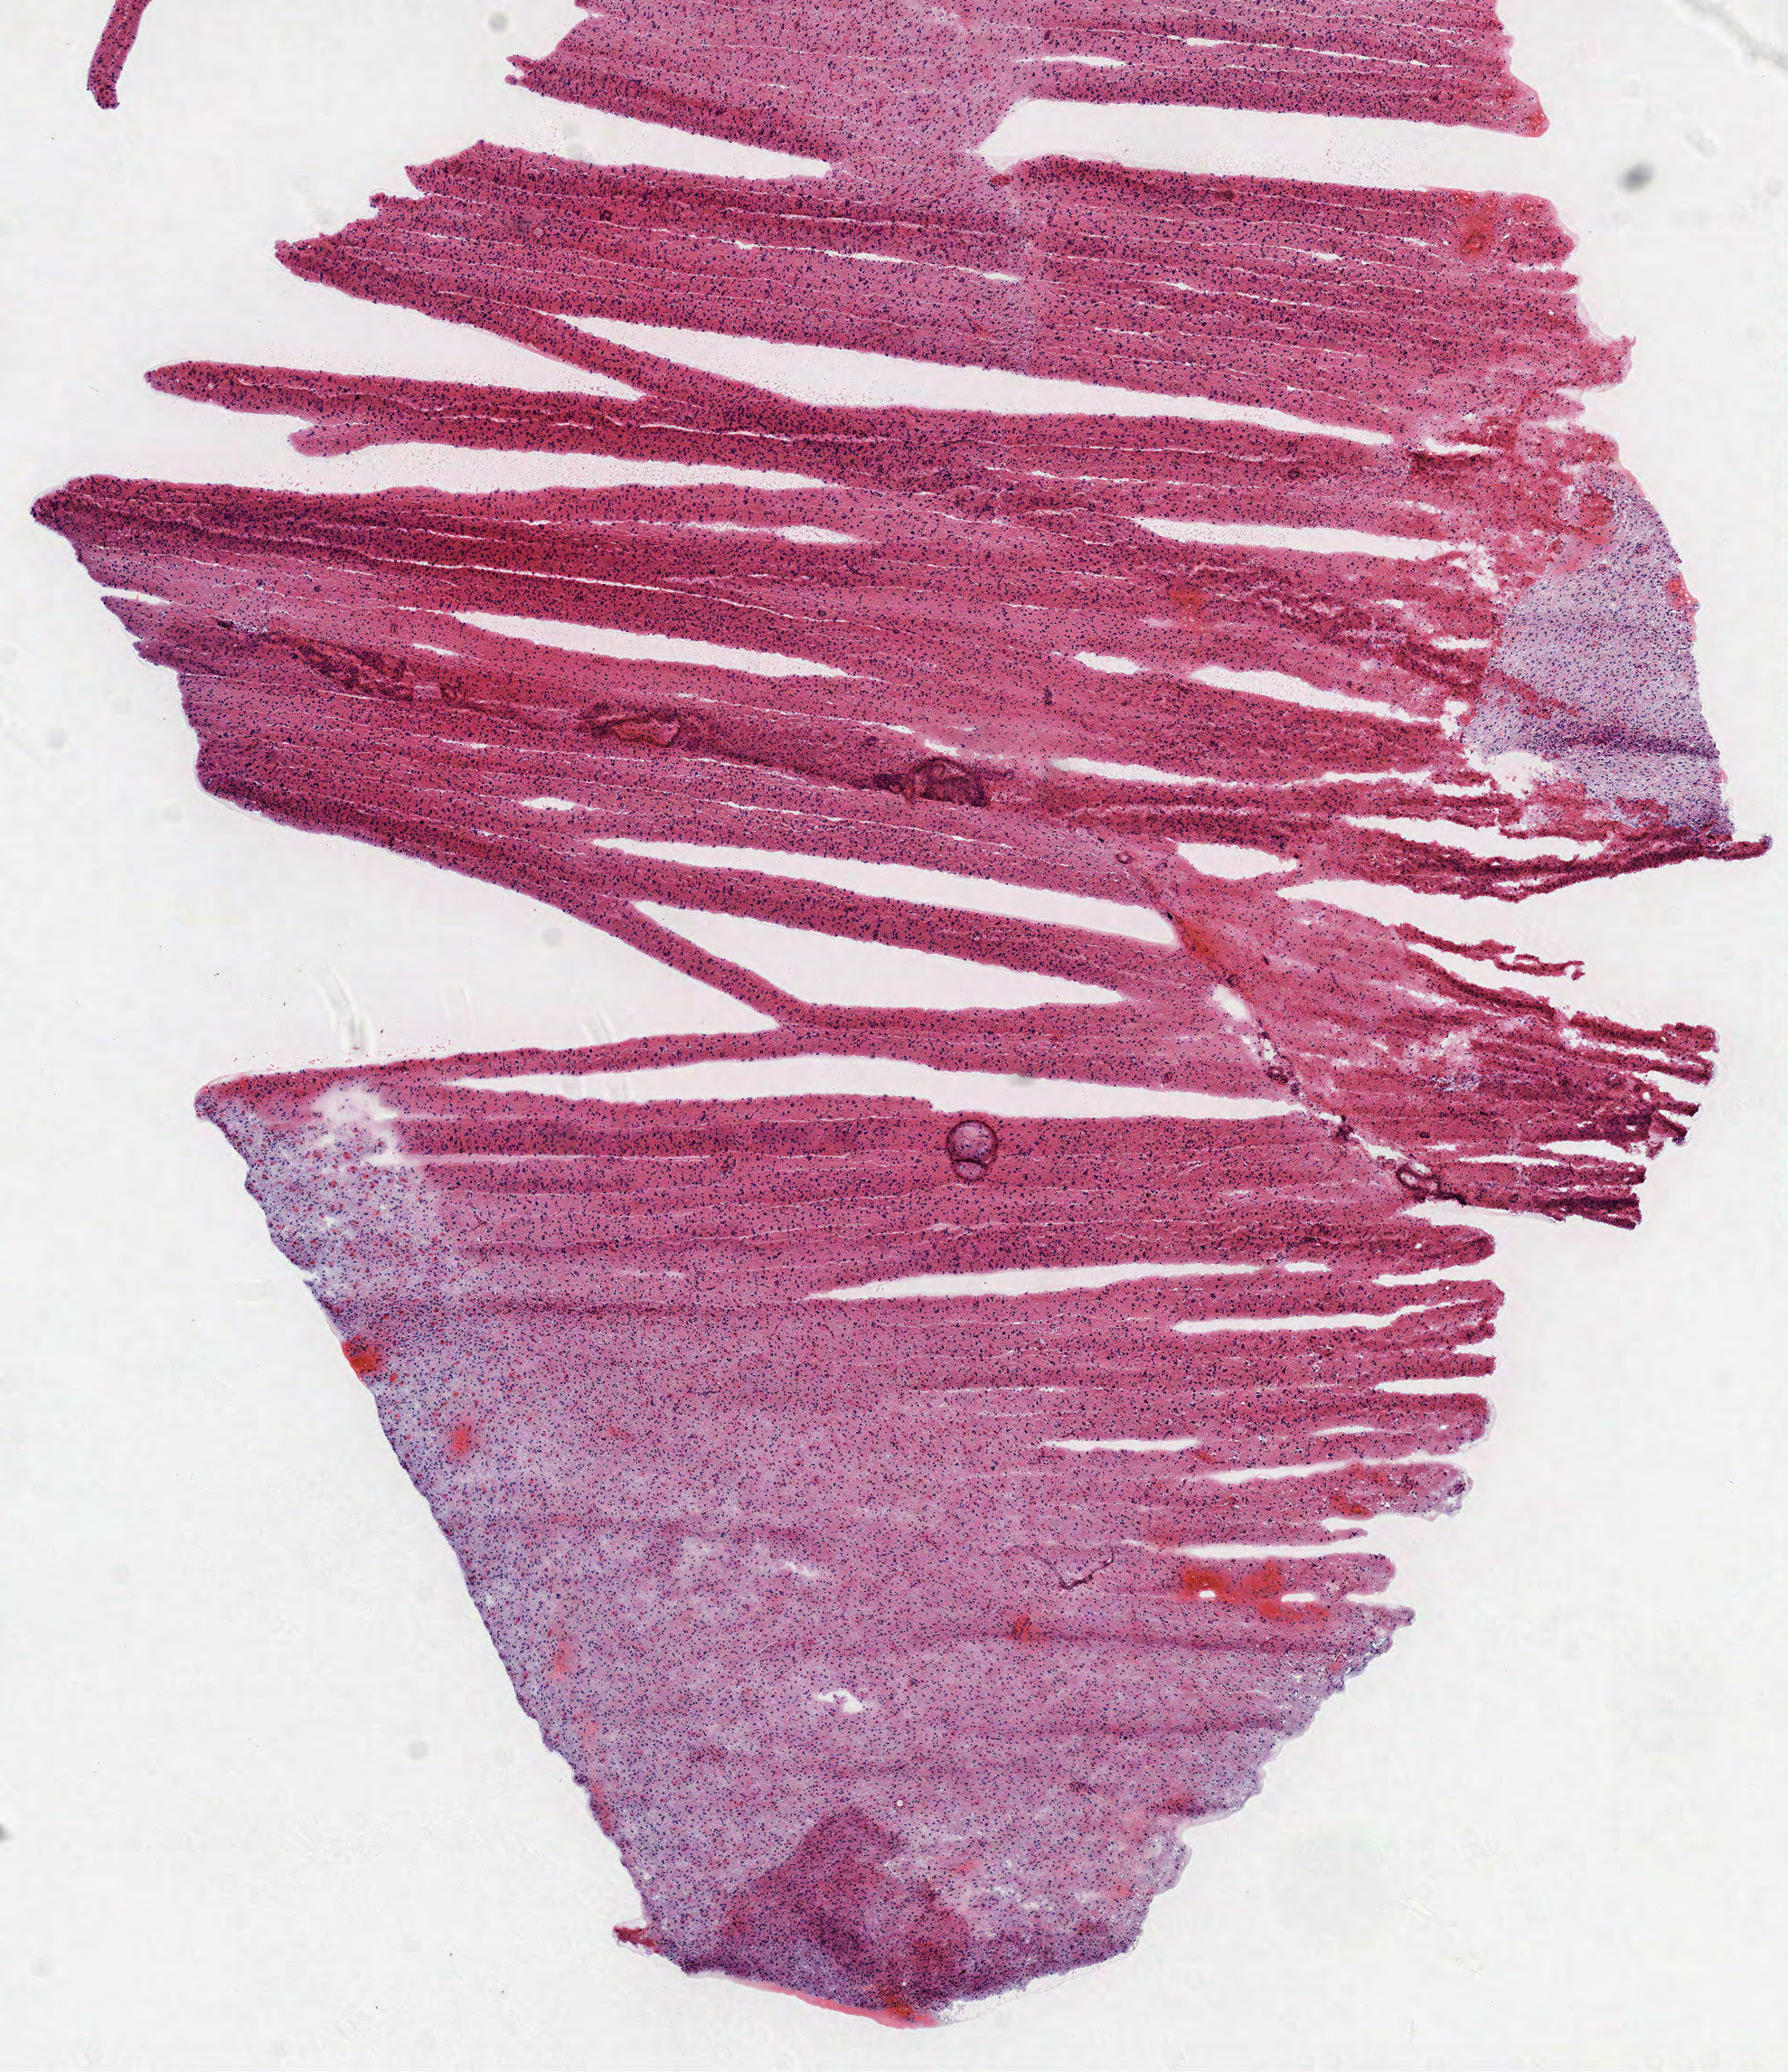
H&E-stained whole-slide image — a low-resolution overview of the entire scanned area, about 8.0 x 9.2 mm, frozen section from the top of the tissue portion, sample: primary tumour, brain. Male patient; age at initial diagnosis 38 years.
Histologic diagnosis: Mixed glioma (cerebrum).